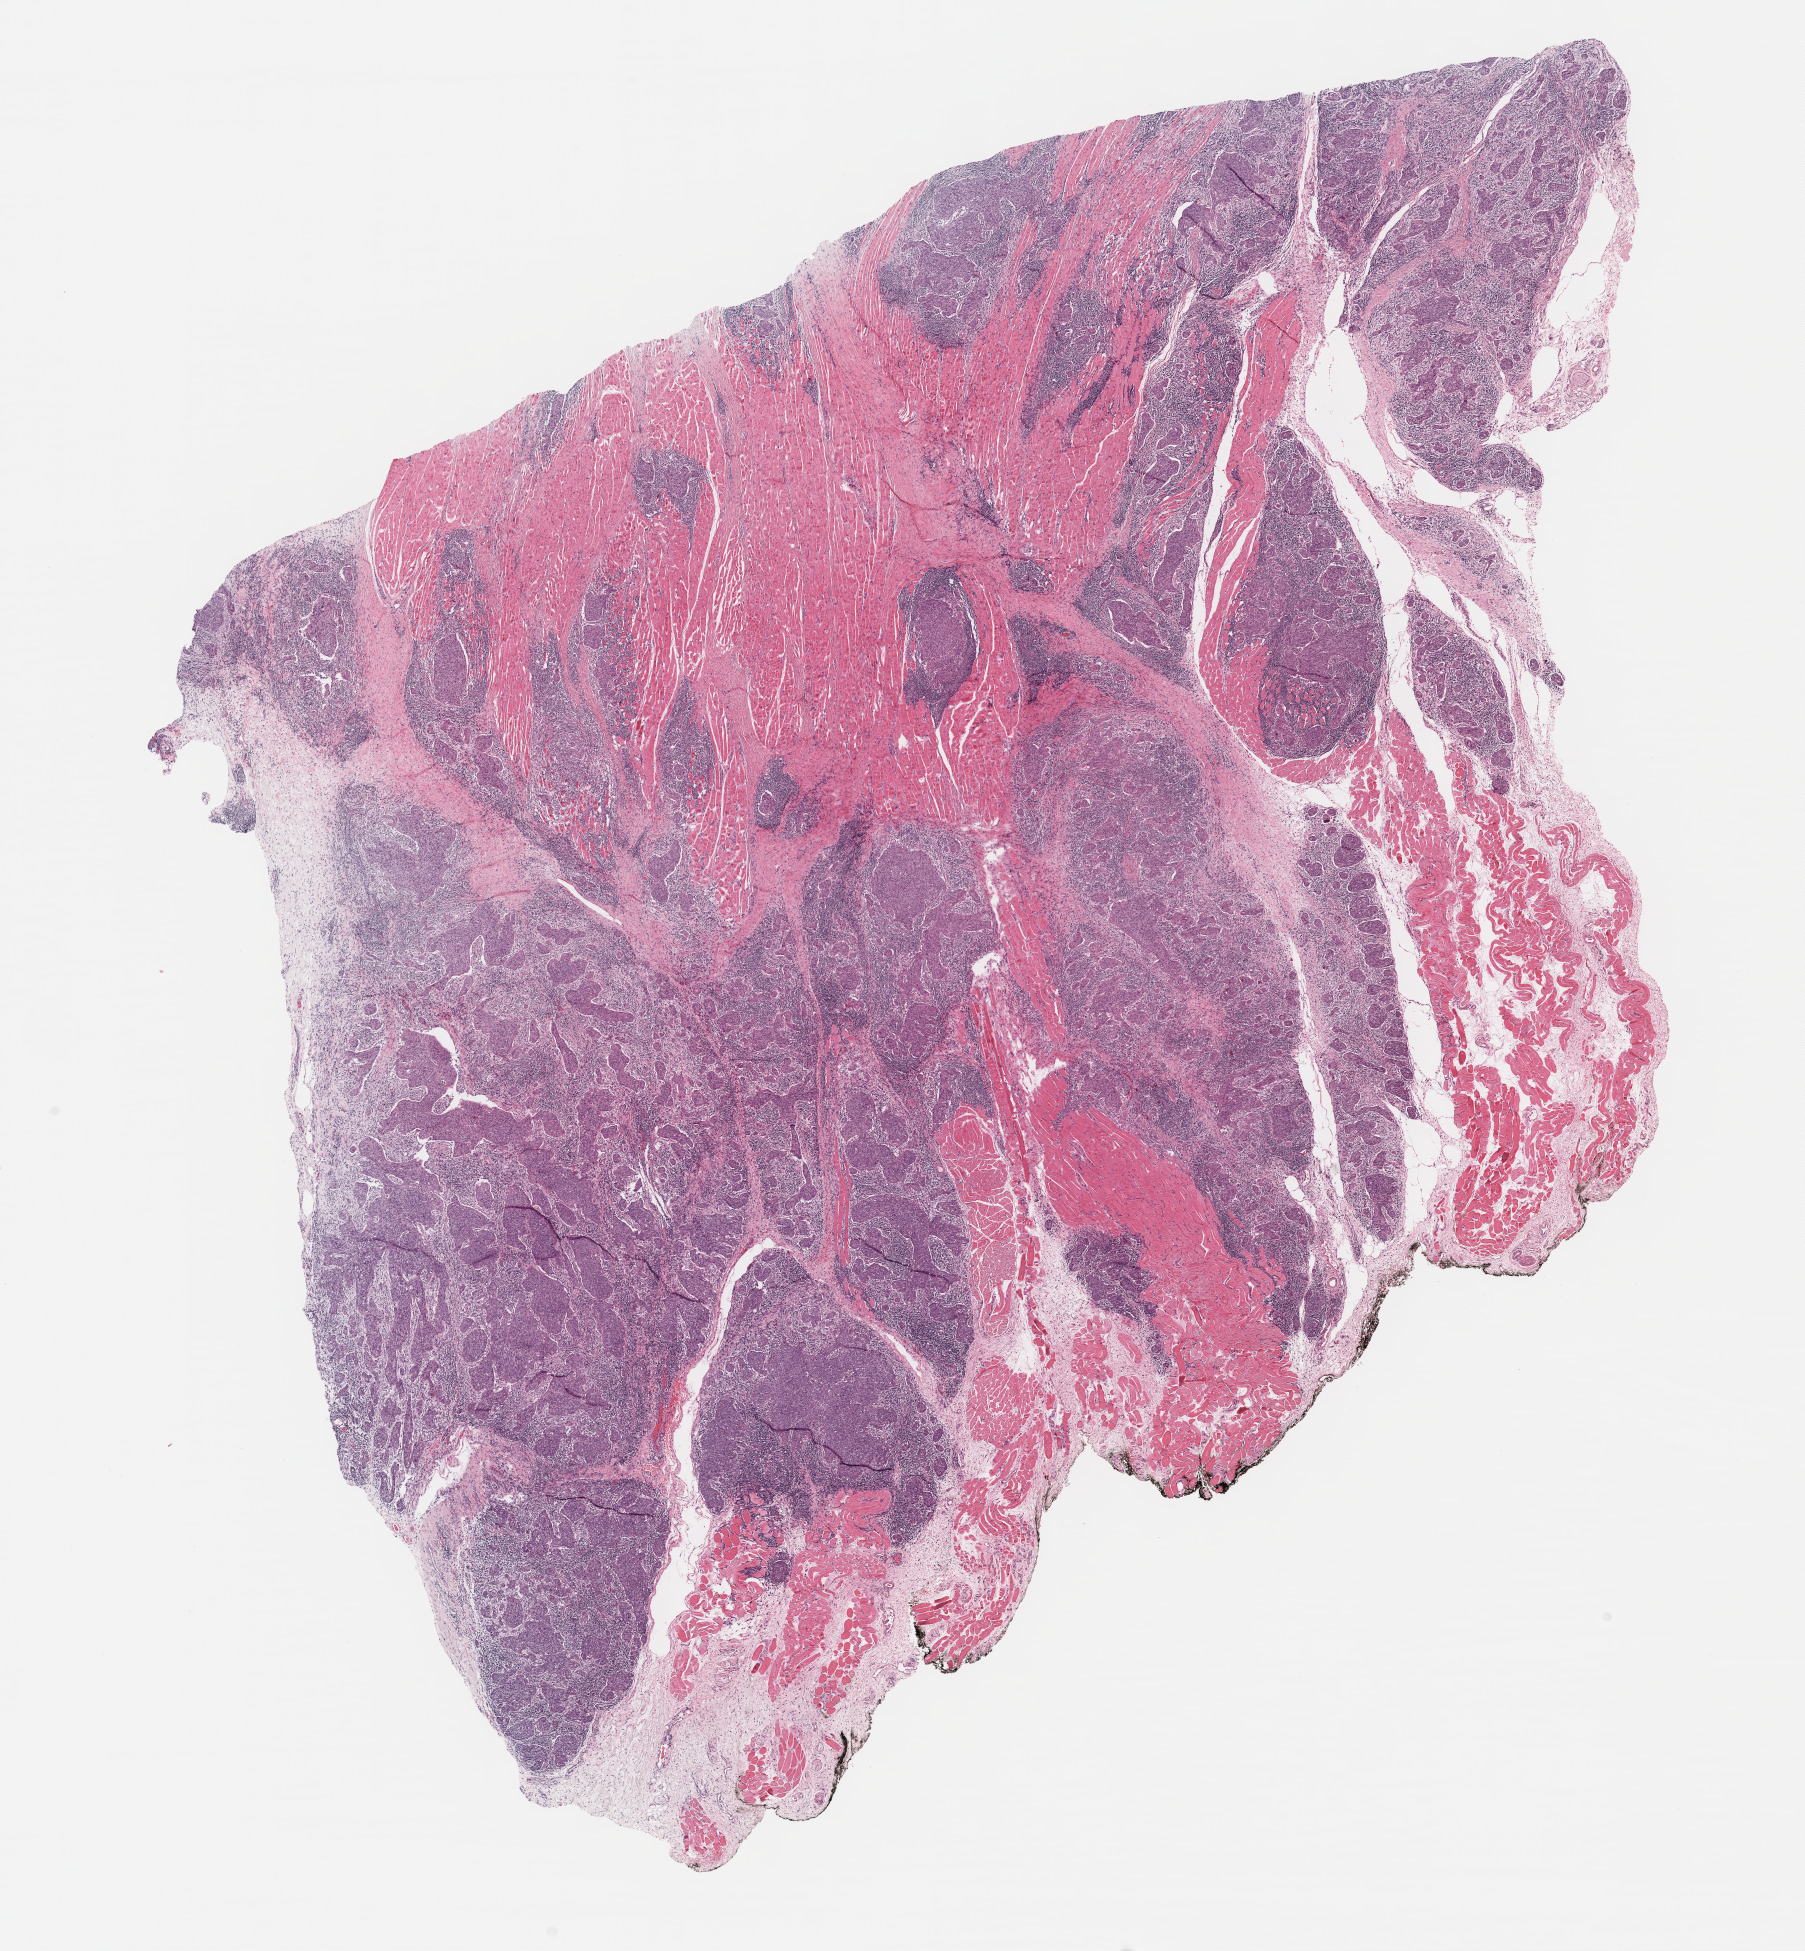
Whole-slide histology image, H&E — shown as a low-resolution overview of the whole scanned area (about 14.6 x 15.8 mm), formalin-fixed paraffin-embedded (FFPE) diagnostic section, primary tumour sample from the head and neck. Male, age 59 years at initial diagnosis. Histologic grade: G2 (moderately differentiated).
Diagnosis: Squamous cell carcinoma, NOS (hypopharynx, NOS). AJCC pathologic stage: IVA (7th edition).